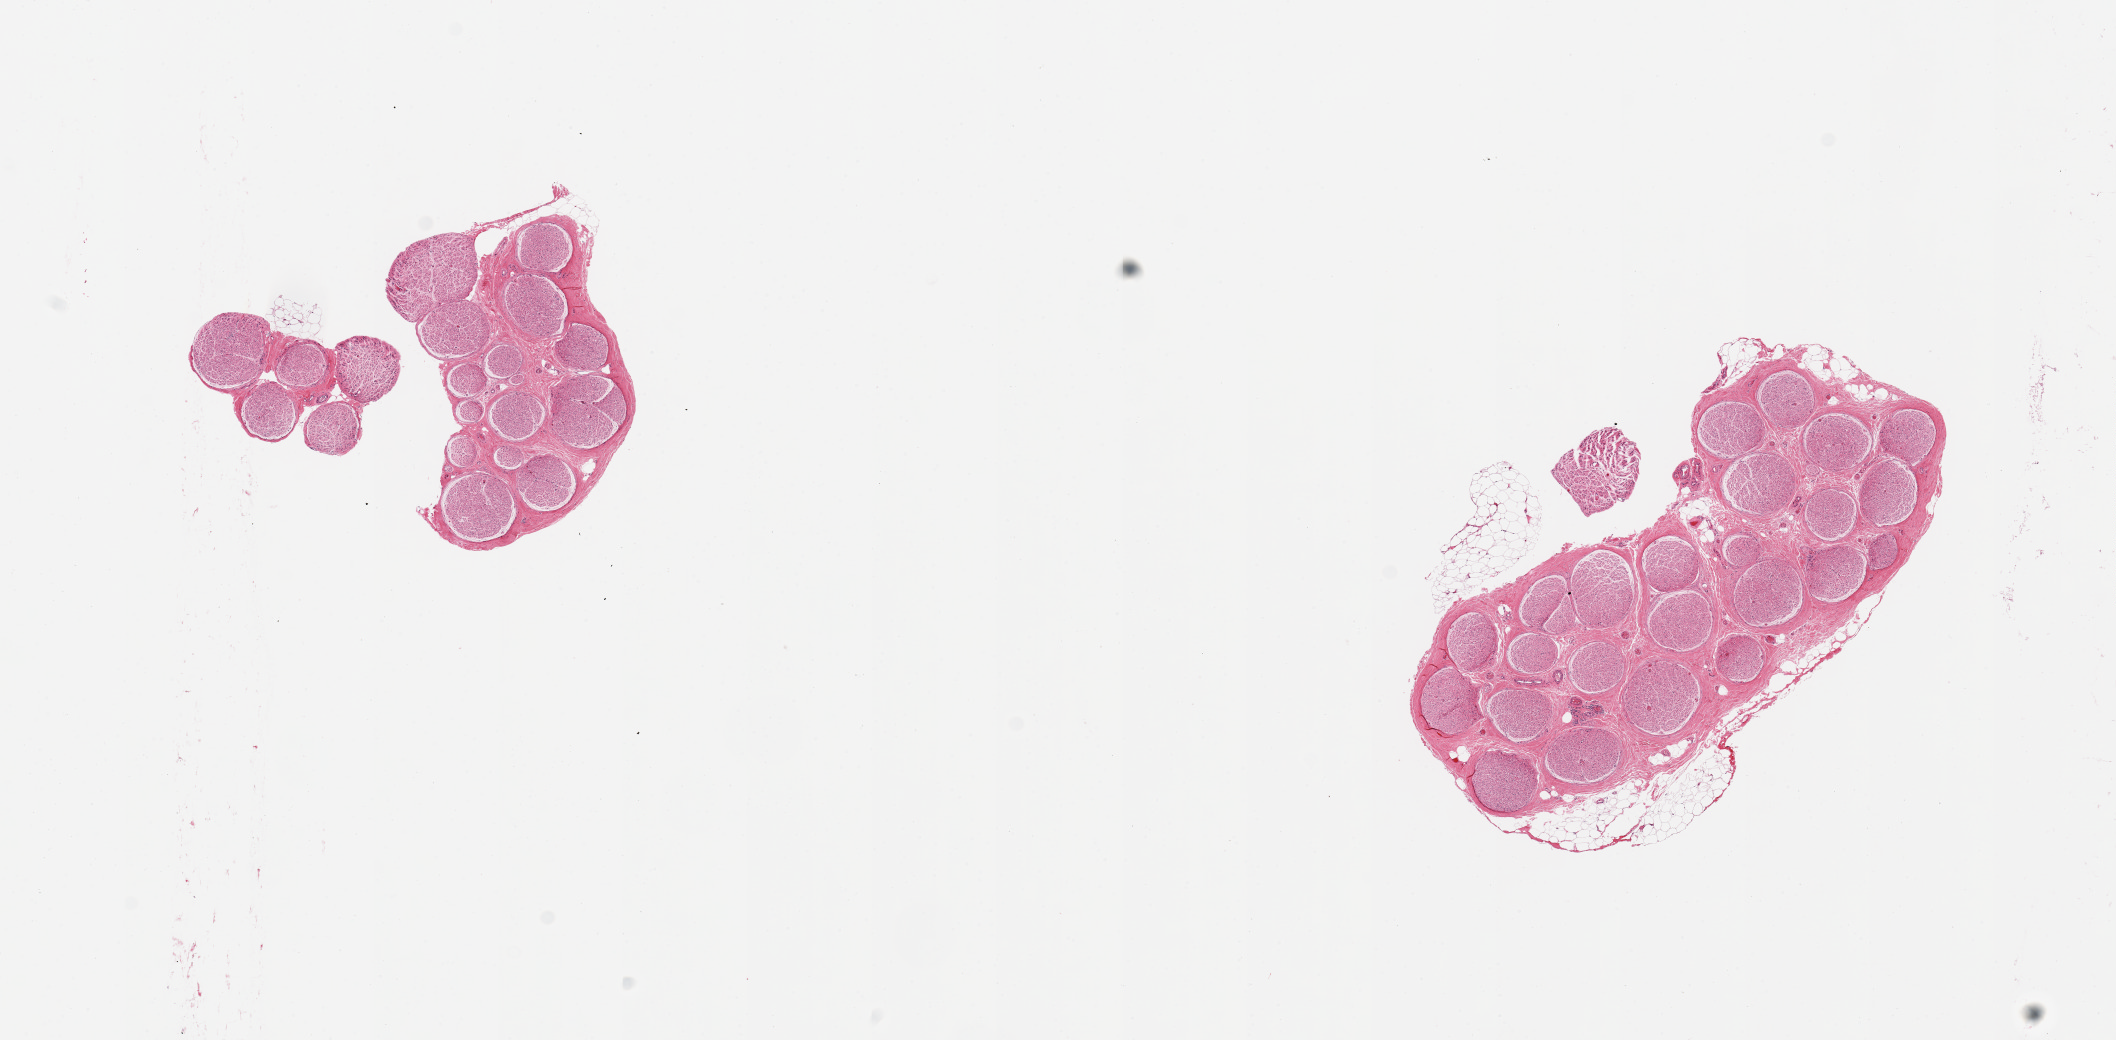
Digitized hematoxylin and eosin (H&E)-stained section, brightfield — shown as a low-resolution overview of the whole scanned area (about 16.7 x 8.2 mm, slide scanned at 20x); PAXgene-fixed paraffin-embedded (PFPE) section; sampled site (target tissue): tibial nerve; donor tissue sample. Donor: female.
• pathologist's review note for this sample: 2 pieces plus fragments; 10% external fat